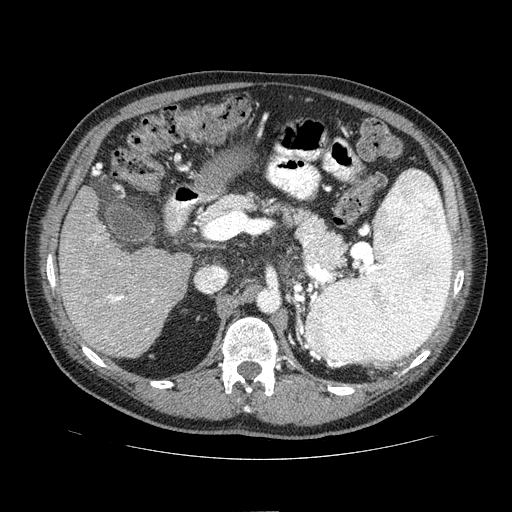
Contrast-enhanced abdominal CT (liver protocol), one axial slice. Position 33 of 81 along the scan axis. Reconstruction kernel STANDARD. One of 2 acquisitions stored at this slice position. Soft-tissue window (W 400 / L 40 HU). 2.5 mm slice thickness. 512 × 512 image matrix, field of view 400 × 400 mm. Case-level facts recorded for this patient, not image findings: diagnosis: hepatocellular carcinoma (patient treated with transarterial chemoembolisation; whether this scan precedes or follows treatment is not stated here); TNM stage (as recorded): Stage-IIIA; Child-Pugh class: A; tumour differentiation: well differentiated; tumour nodularity: multinodular.
Annotated regions visible in this slice (semi-automatically segmented with operator editing):
- liver parenchyma outside the tumour (the mass and vessels are separate outlines, so this box may not span the whole liver): box from (x=58, y=186) to (x=192, y=358) px
- liver vessels: (x=83, y=237)–(x=155, y=338)